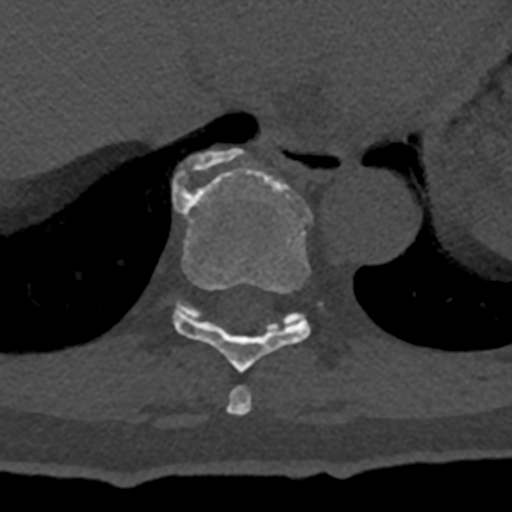
CT including the spine, one axial slice. Slice 644 of 797 in the series (ordered by position). Reconstruction kernel Br40s/3. 120 kVp. Bone window (W 1800 / L 400 HU). 512 × 512 image matrix, field of view 160 × 160 mm. Male patient, age 74 years. From the clinical record (not read from this slice): primary cancer: renal; vertebrae with lytic lesions (as recorded): T10, L1, L2, L3, L4, L5.
Outlined on this slice (semi-automatically segmented with operator editing):
- T10 vertebra: box from (x=172, y=148) to (x=303, y=328) px
- T8 vertebra: (x=227, y=386)–(x=252, y=415)
- T9 vertebra: (x=173, y=169)–(x=313, y=372)